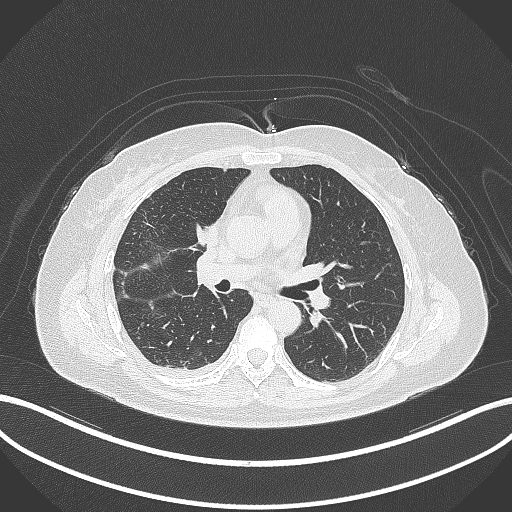
Chest CT, one axial slice. Slice 151 of 305 in the series (ordered by position). Lung window (W 1500 / L -600 HU). 1 mm slice thickness. 512 × 512 image matrix, field of view 400 × 400 mm. Patient: female, 52 years. Case-level facts recorded for this patient, not image findings: clinical TNM (as recorded): T3 N1 M1.
Outlined on this slice (bounding box drawn by a radiologist):
- lung tumour (recorded histology: adenocarcinoma): bounding box [x1, y1, x2, y2] px = [192, 214, 223, 251]